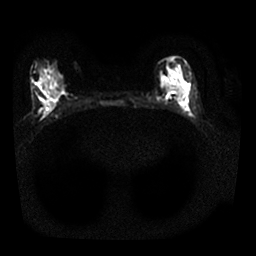
Breast MRI, one axial slice; slice 11 of 25 in the series (ordered by position); diffusion-weighted series; image 2 of 4 stored at this slice position (different b-values; order by instance number); 1.5 T; 4 mm slice thickness; 256 × 256 image matrix, field of view 310 × 310 mm. Female patient.
Structures marked on this image (outlined manually by an expert reader):
- tumour on diffusion-weighted imaging: bounding box <178,97,183,101> (left, top, right, bottom; pixels)